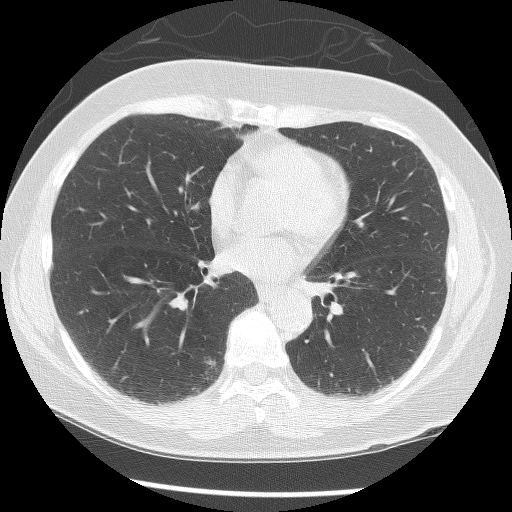
Low-dose screening chest CT, axial slice; baseline annual screen; lung window (W 1500 / L -600 HU); 2.5 mm slice thickness; lung (sharp) reconstruction kernel (BONE); slice 66 of 125 in the series. Female participant, aged 56 years at enrolment.
Lesion marked by an expert reader, bounding box <191,349,233,388> (left, top, right, bottom; pixels). The exam's reader record, not a measurement of the box and not confirmed to be the same lesion: non-calcified nodule or mass ≥4 mm, right lower lobe, 8 × 7 mm, smooth margins, soft tissue attenuation. Participant outcome: lung cancer diagnosed 167 days after this screen — adenocarcinoma, NOS, right lower lobe, poorly differentiated (G3), stage IA (AJCC 6th edition), 12 mm at pathology.